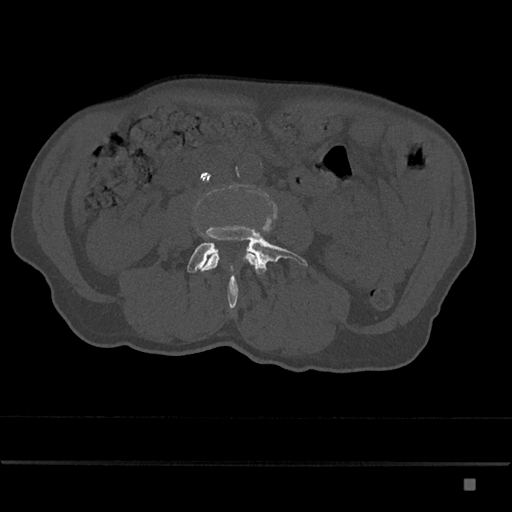
CT including the spine, one axial slice; position 363 of 797 along the scan axis; reconstruction kernel Br40s/3; 120 kVp; bone window (W 1800 / L 400 HU); 0.5 mm slice thickness; 512 × 512 image matrix, field of view 390 × 390 mm. Male patient, age 72 years. From the clinical record (not read from this slice): primary cancer: prostate.
Structures marked on this image (semi-automatically segmented with operator editing):
- L3 vertebra: bounding box <202,254,258,271> (left, top, right, bottom; pixels)
- L4 vertebra: <187,181,308,308>